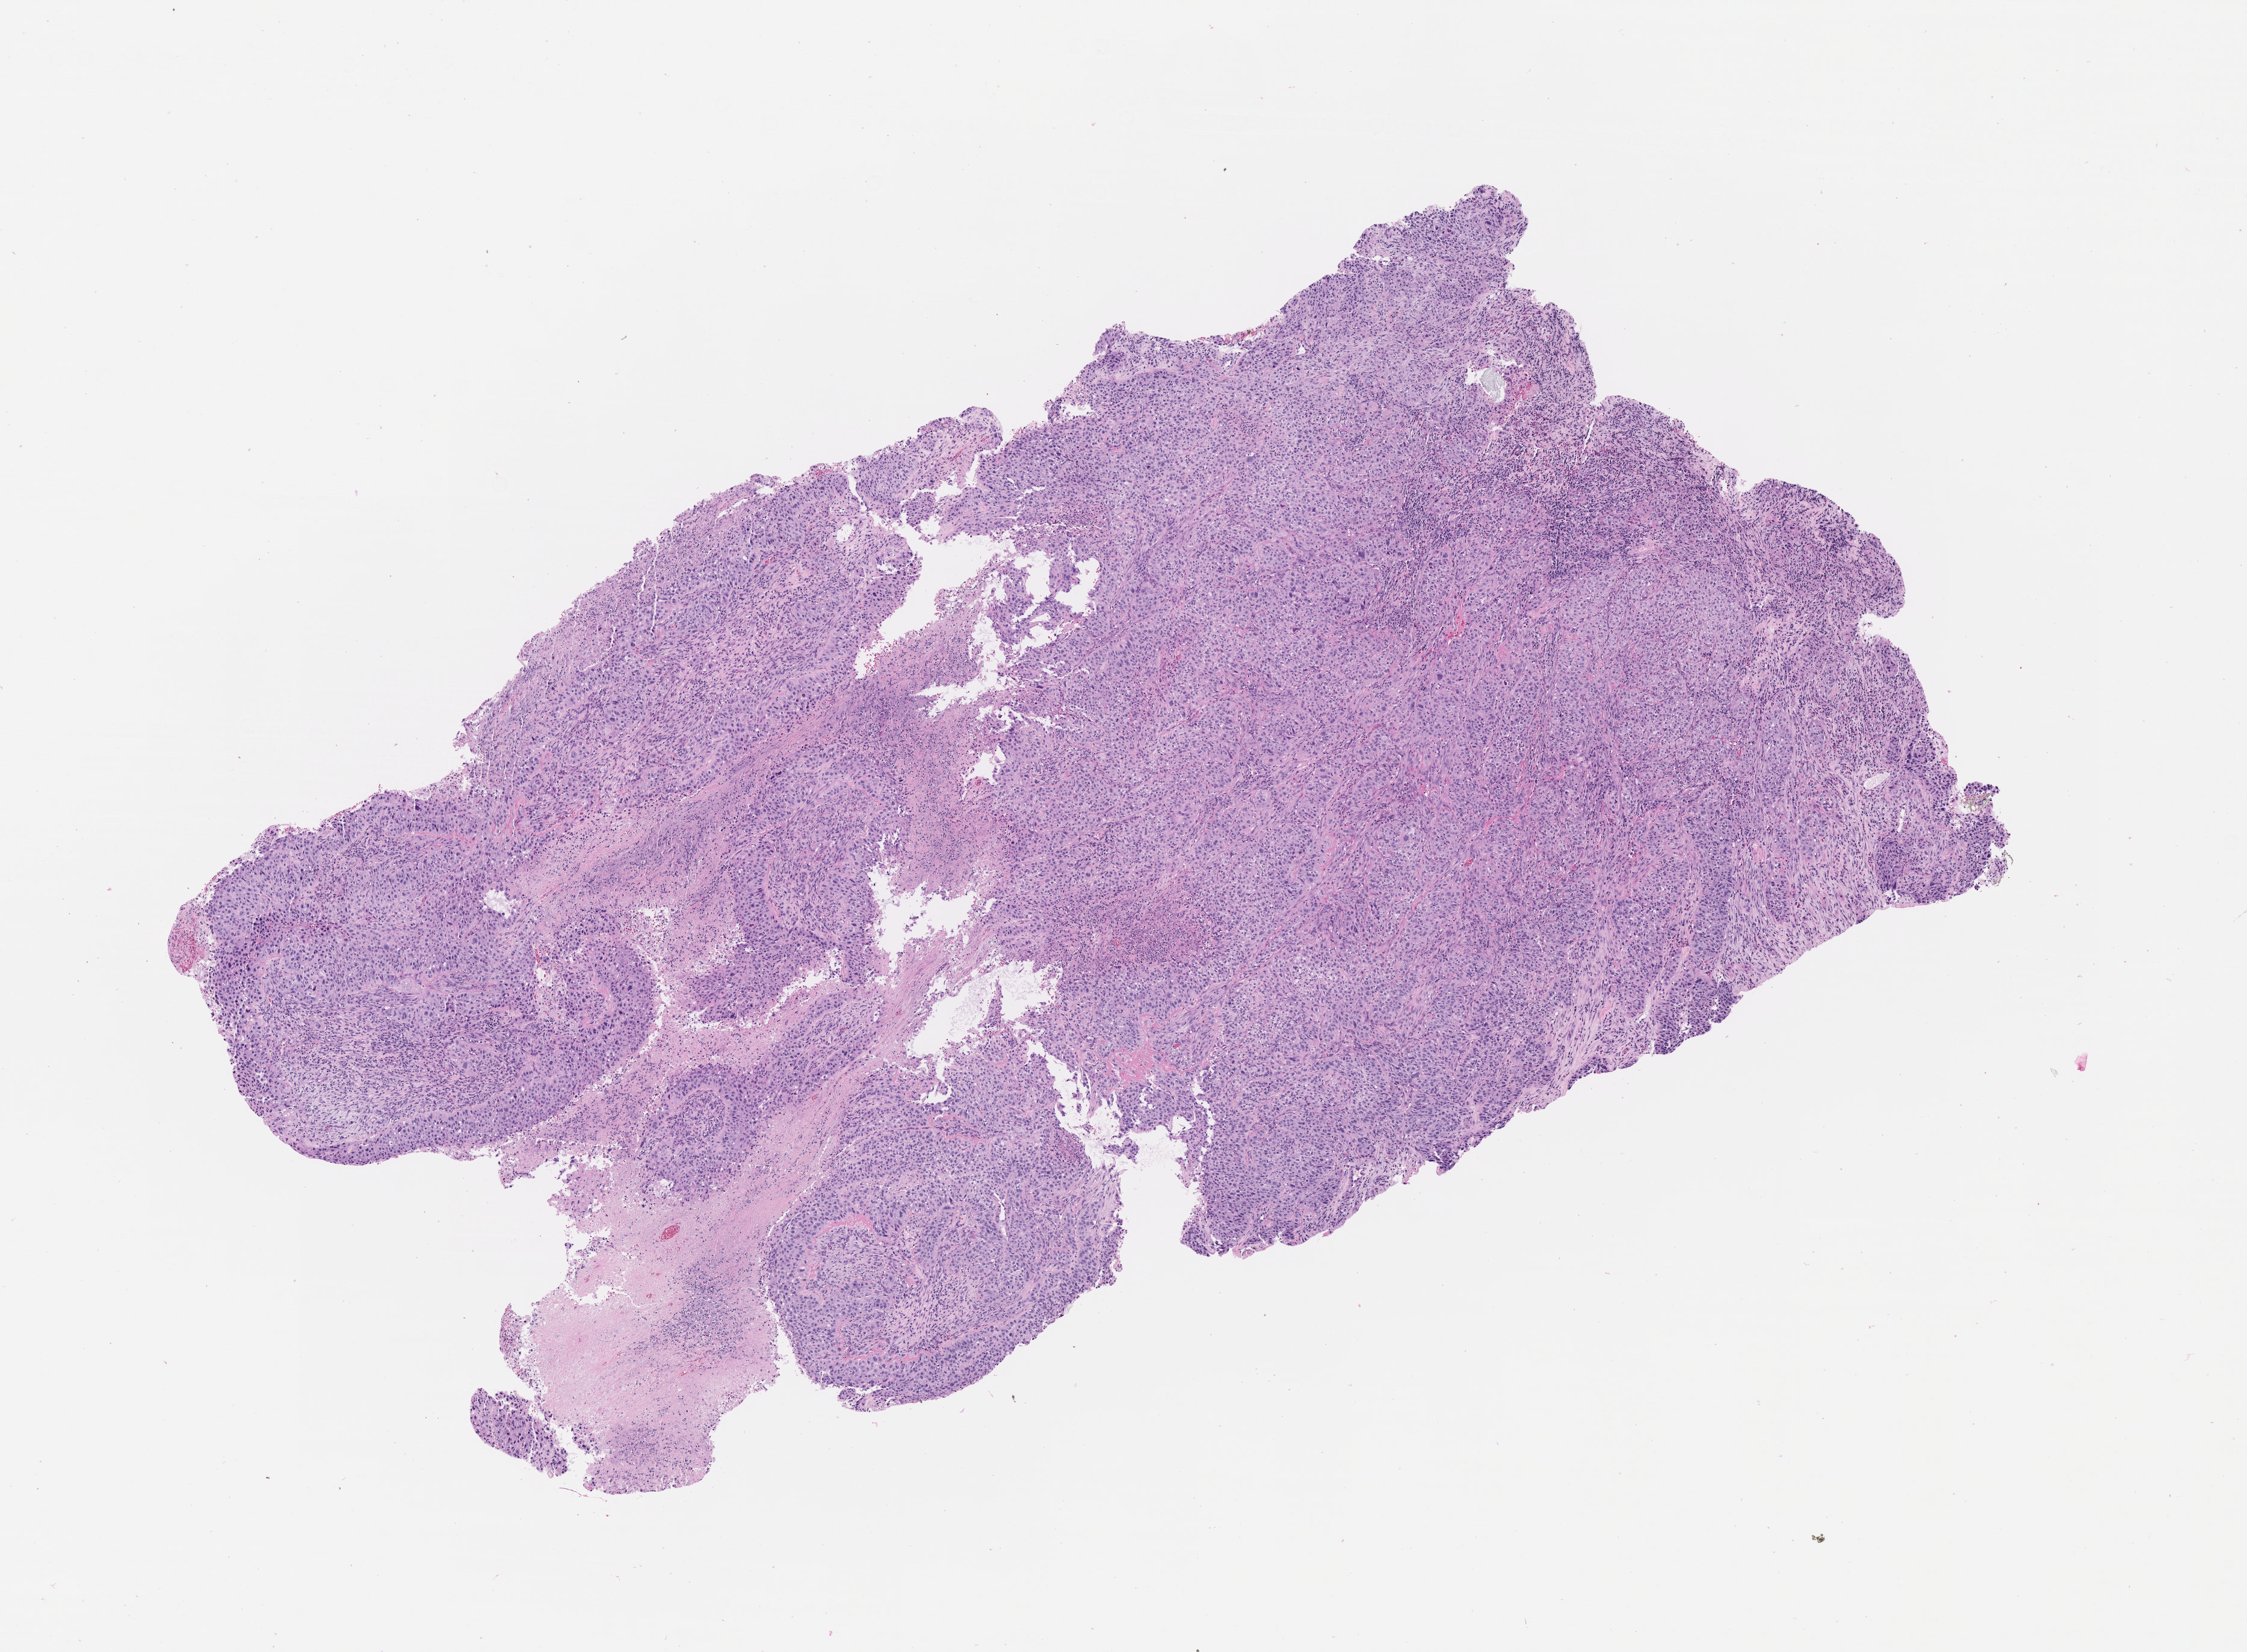
Whole-slide image, H&E stain, shown as a low-resolution overview of the whole scanned area (about 7.5 x 5.5 mm). Tumor tissue. Anatomic site: cervix. Patient: female, age 48 years.
- histologic diagnosis: Squamous cell carcinoma, large cell, nonkeratinizing, NOS